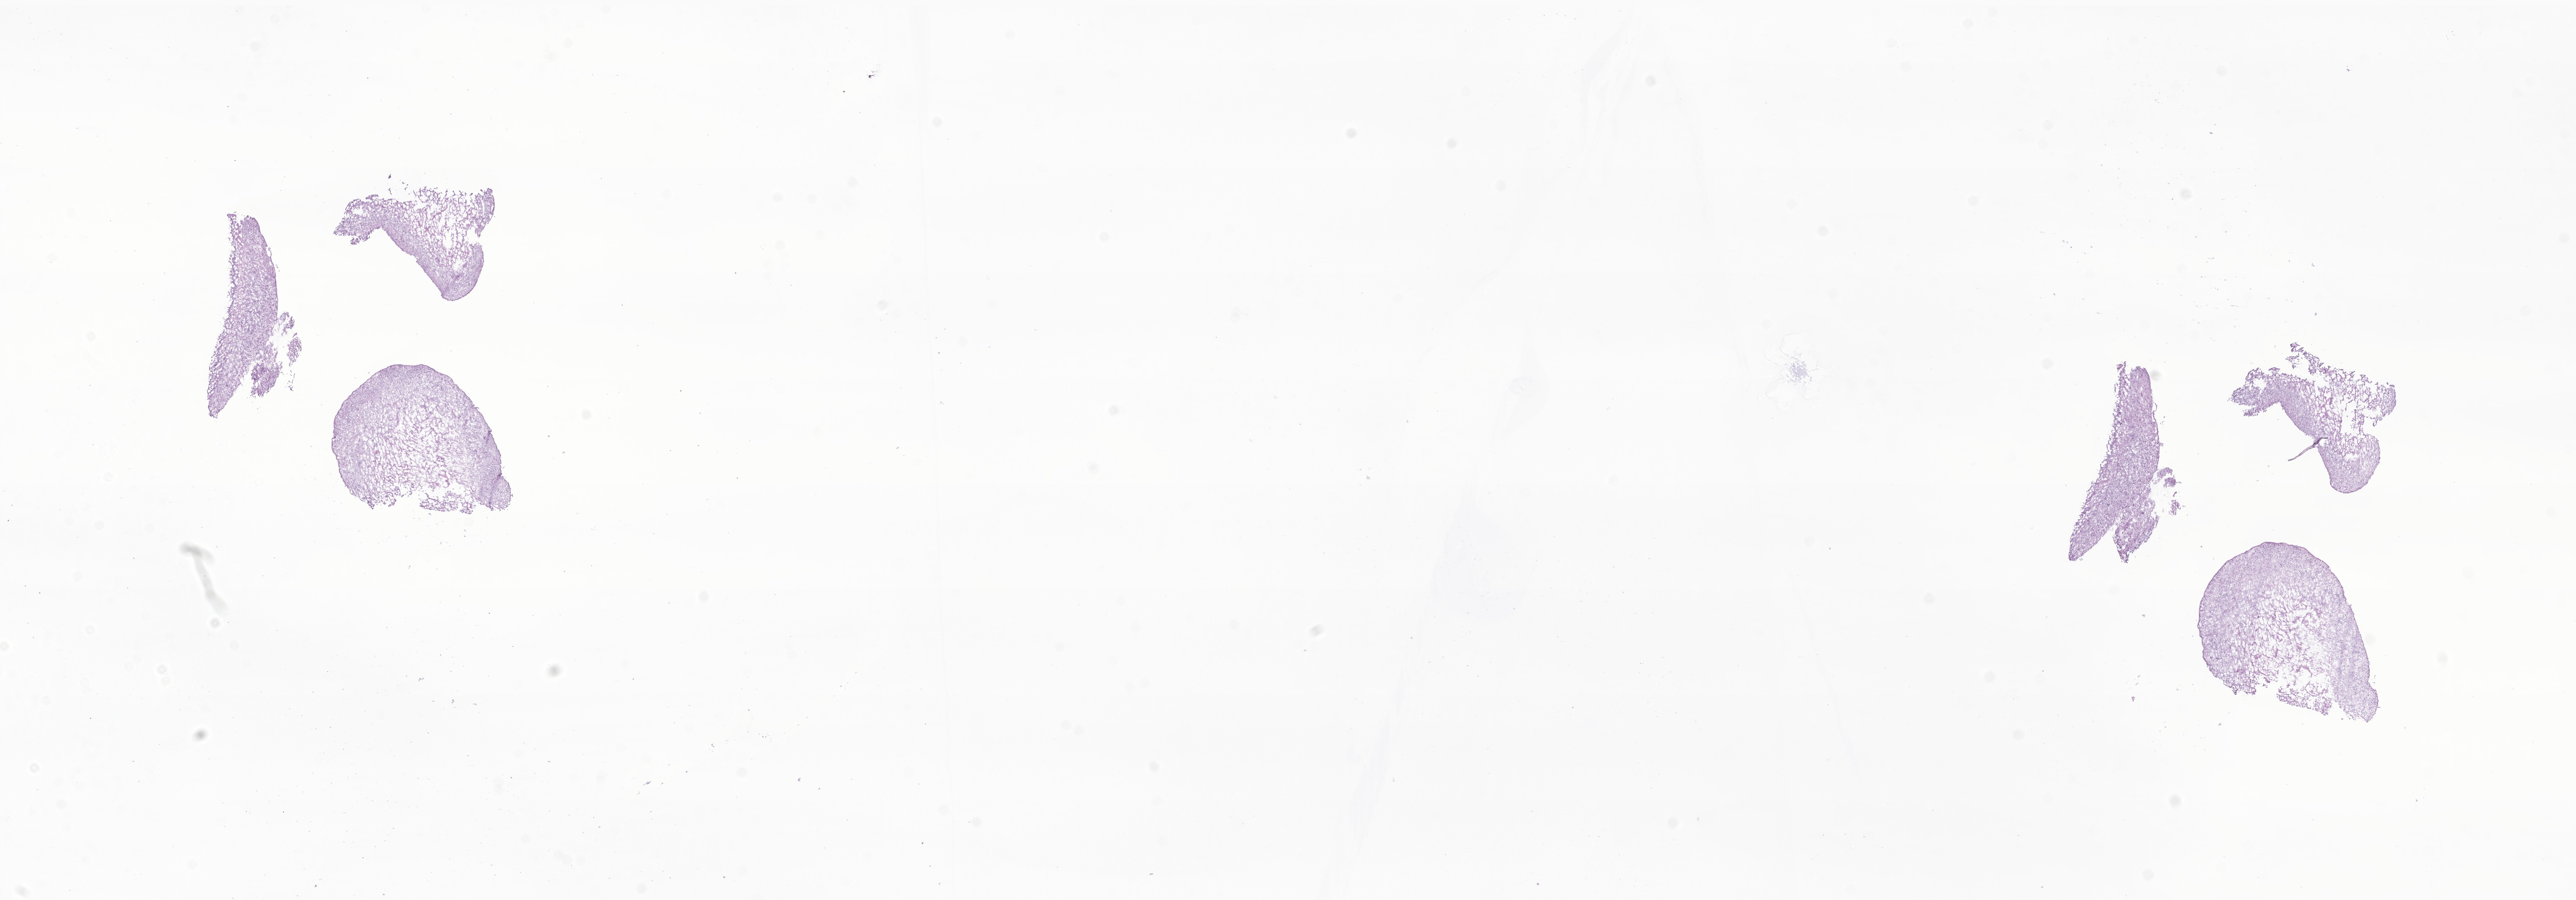
Whole-slide image, haematoxylin and eosin stain of tumor tissue from the brain, whole scanned area (about 26.1 x 9.1 mm) shown as a low-resolution overview; frozen section. Patient: male, age 854 days (about 2.3 years).
Diagnosis: Ependymoma, NOS.